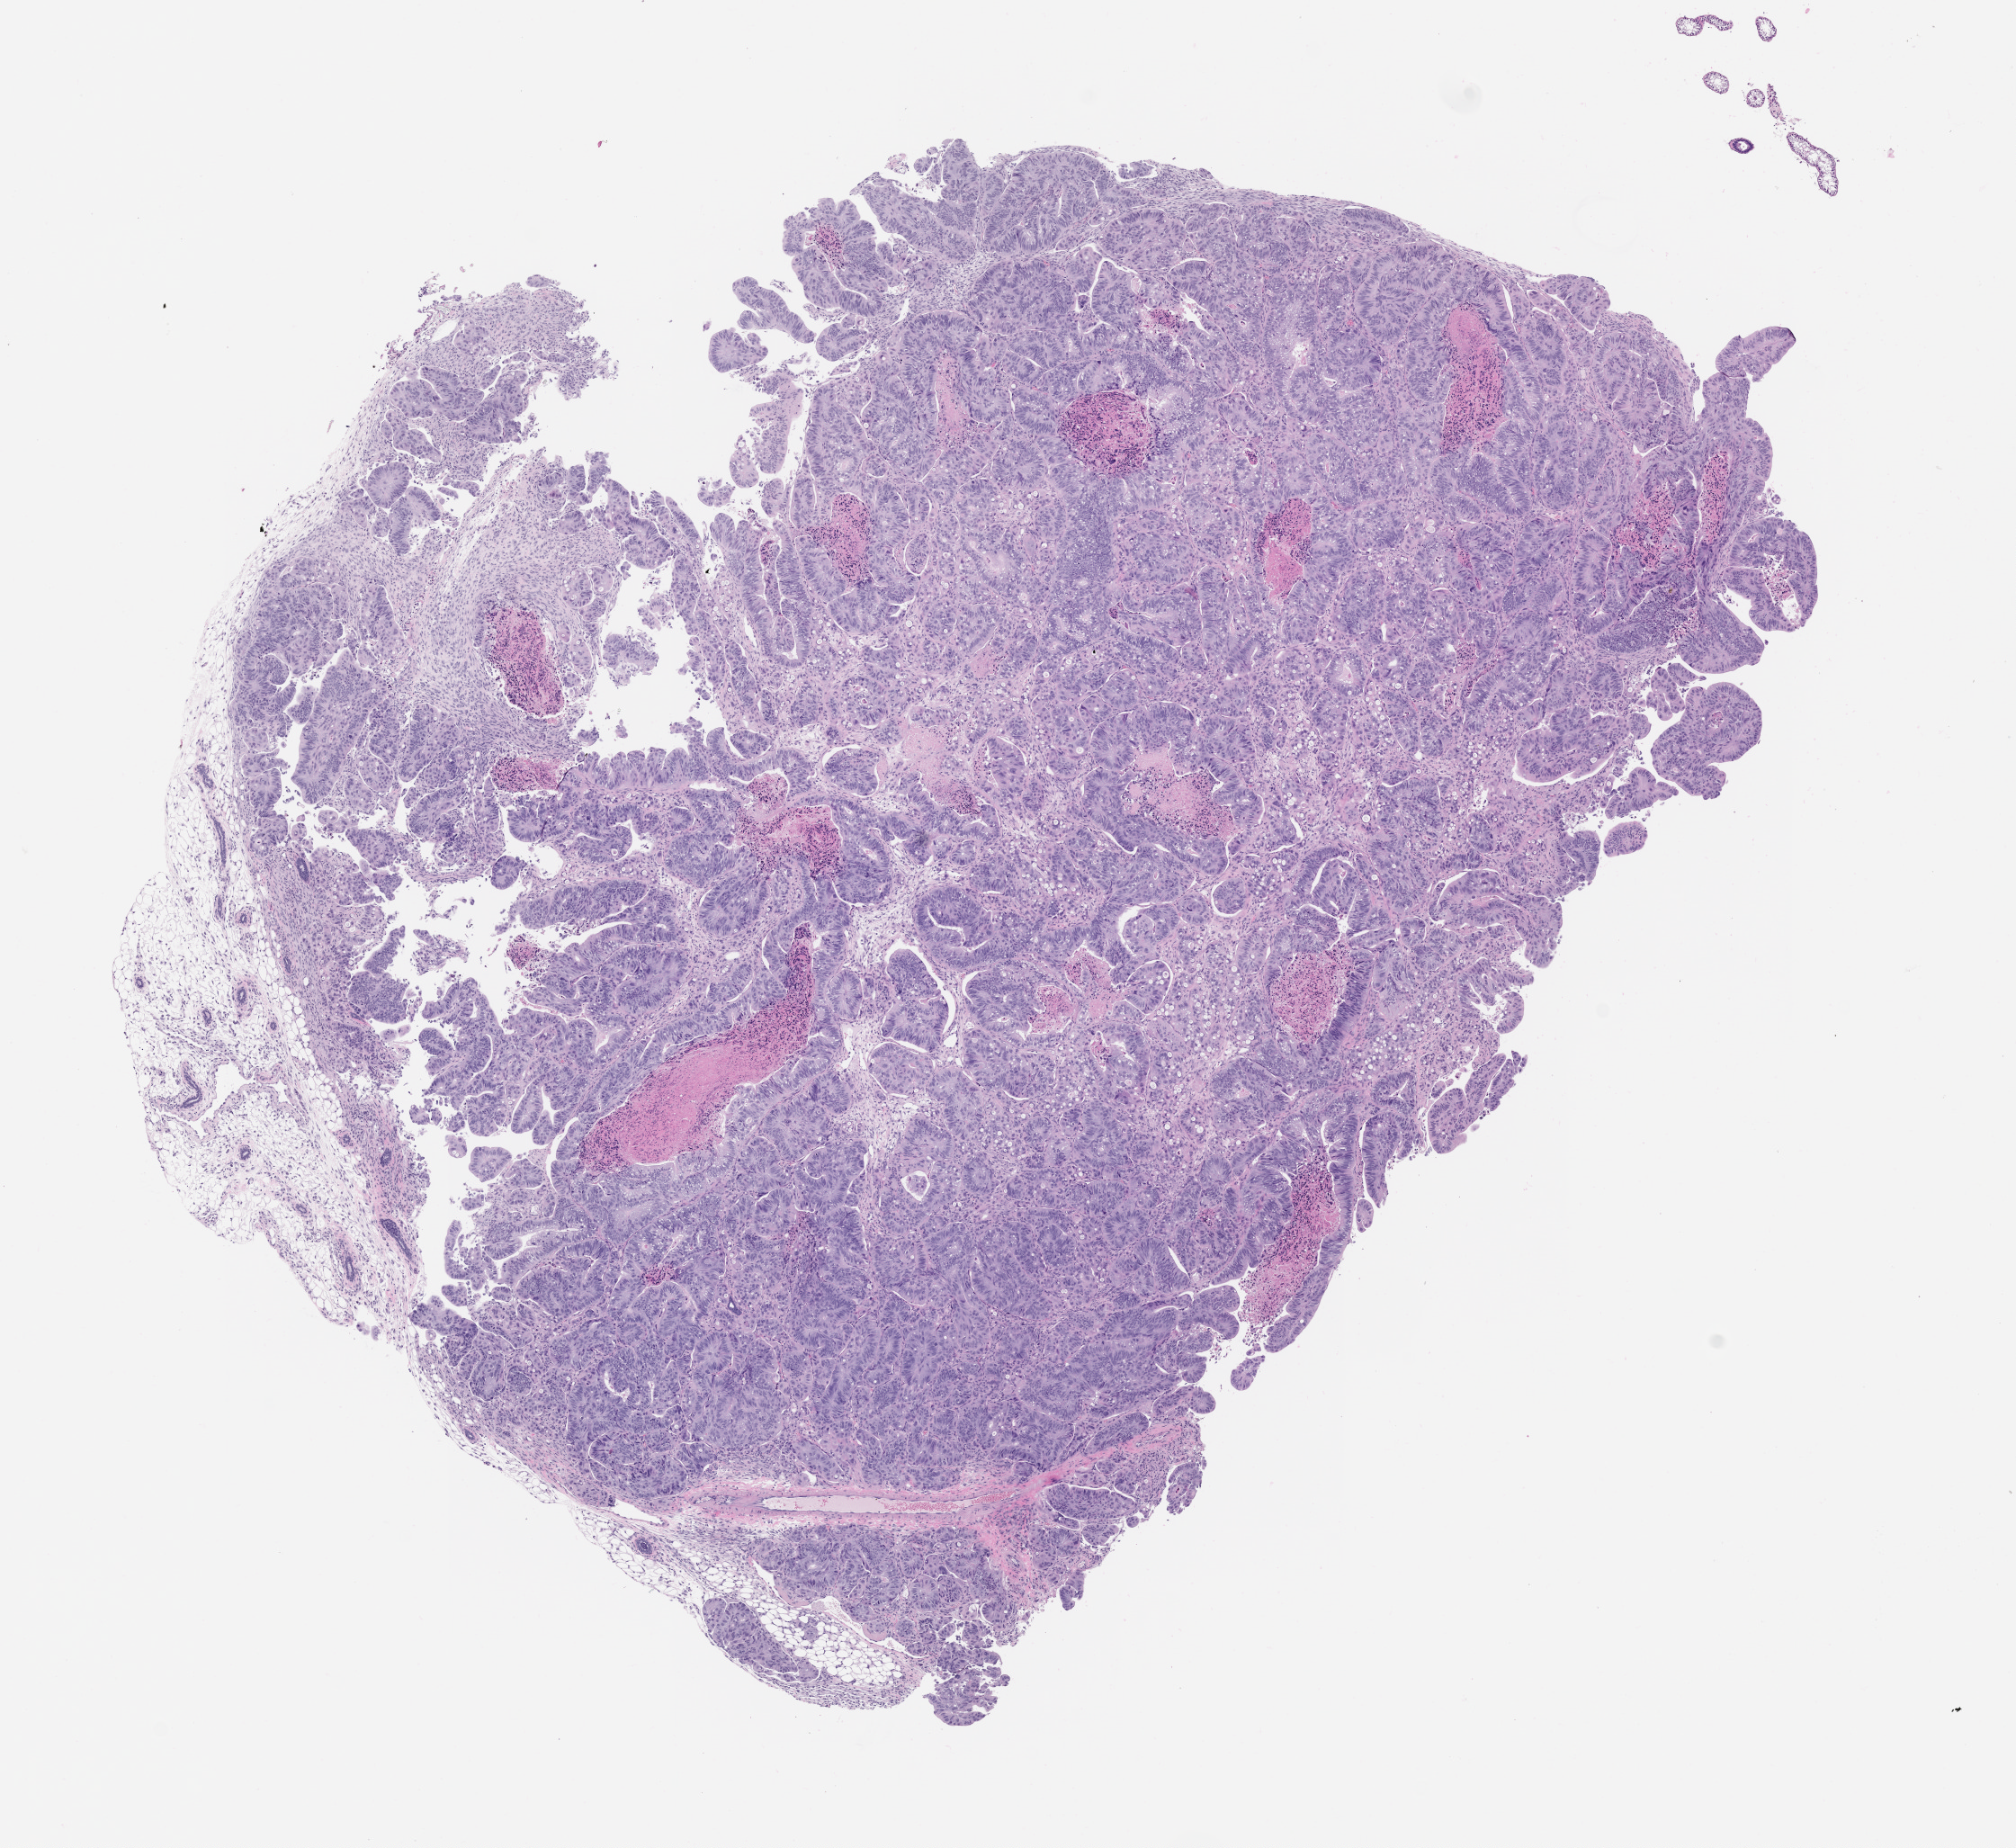
Haematoxylin and eosin whole-slide image of a patient-derived xenograft (PDX) tumor grown in a mouse, passage 3 — low-resolution overview of the scanned area, about 9.0 x 8.3 mm; formalin-fixed paraffin-embedded section; tumor site category: colon.
Originating patient diagnosis: Colon Adenocarcinoma.